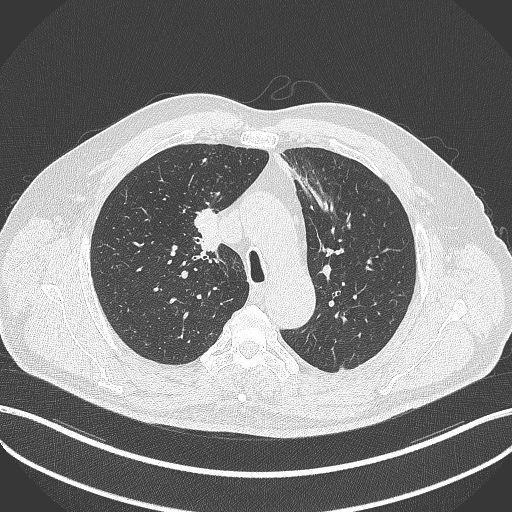
Chest CT, one axial slice; slice 278 of 411 in the series (ordered by position); reconstruction kernel B70f; 120 kVp; lung window (W 1500 / L -600 HU); 1 mm slice thickness; 512 × 512 image matrix. Male patient, age 60 years. From the clinical record (not read from this slice): clinical TNM (as recorded): T1b N1 M0.
Annotated regions visible in this slice (rectangle marked by the reading radiologist):
- lung tumour (recorded histology: squamous cell carcinoma): bounding box [x1, y1, x2, y2] px = [194, 207, 224, 256]